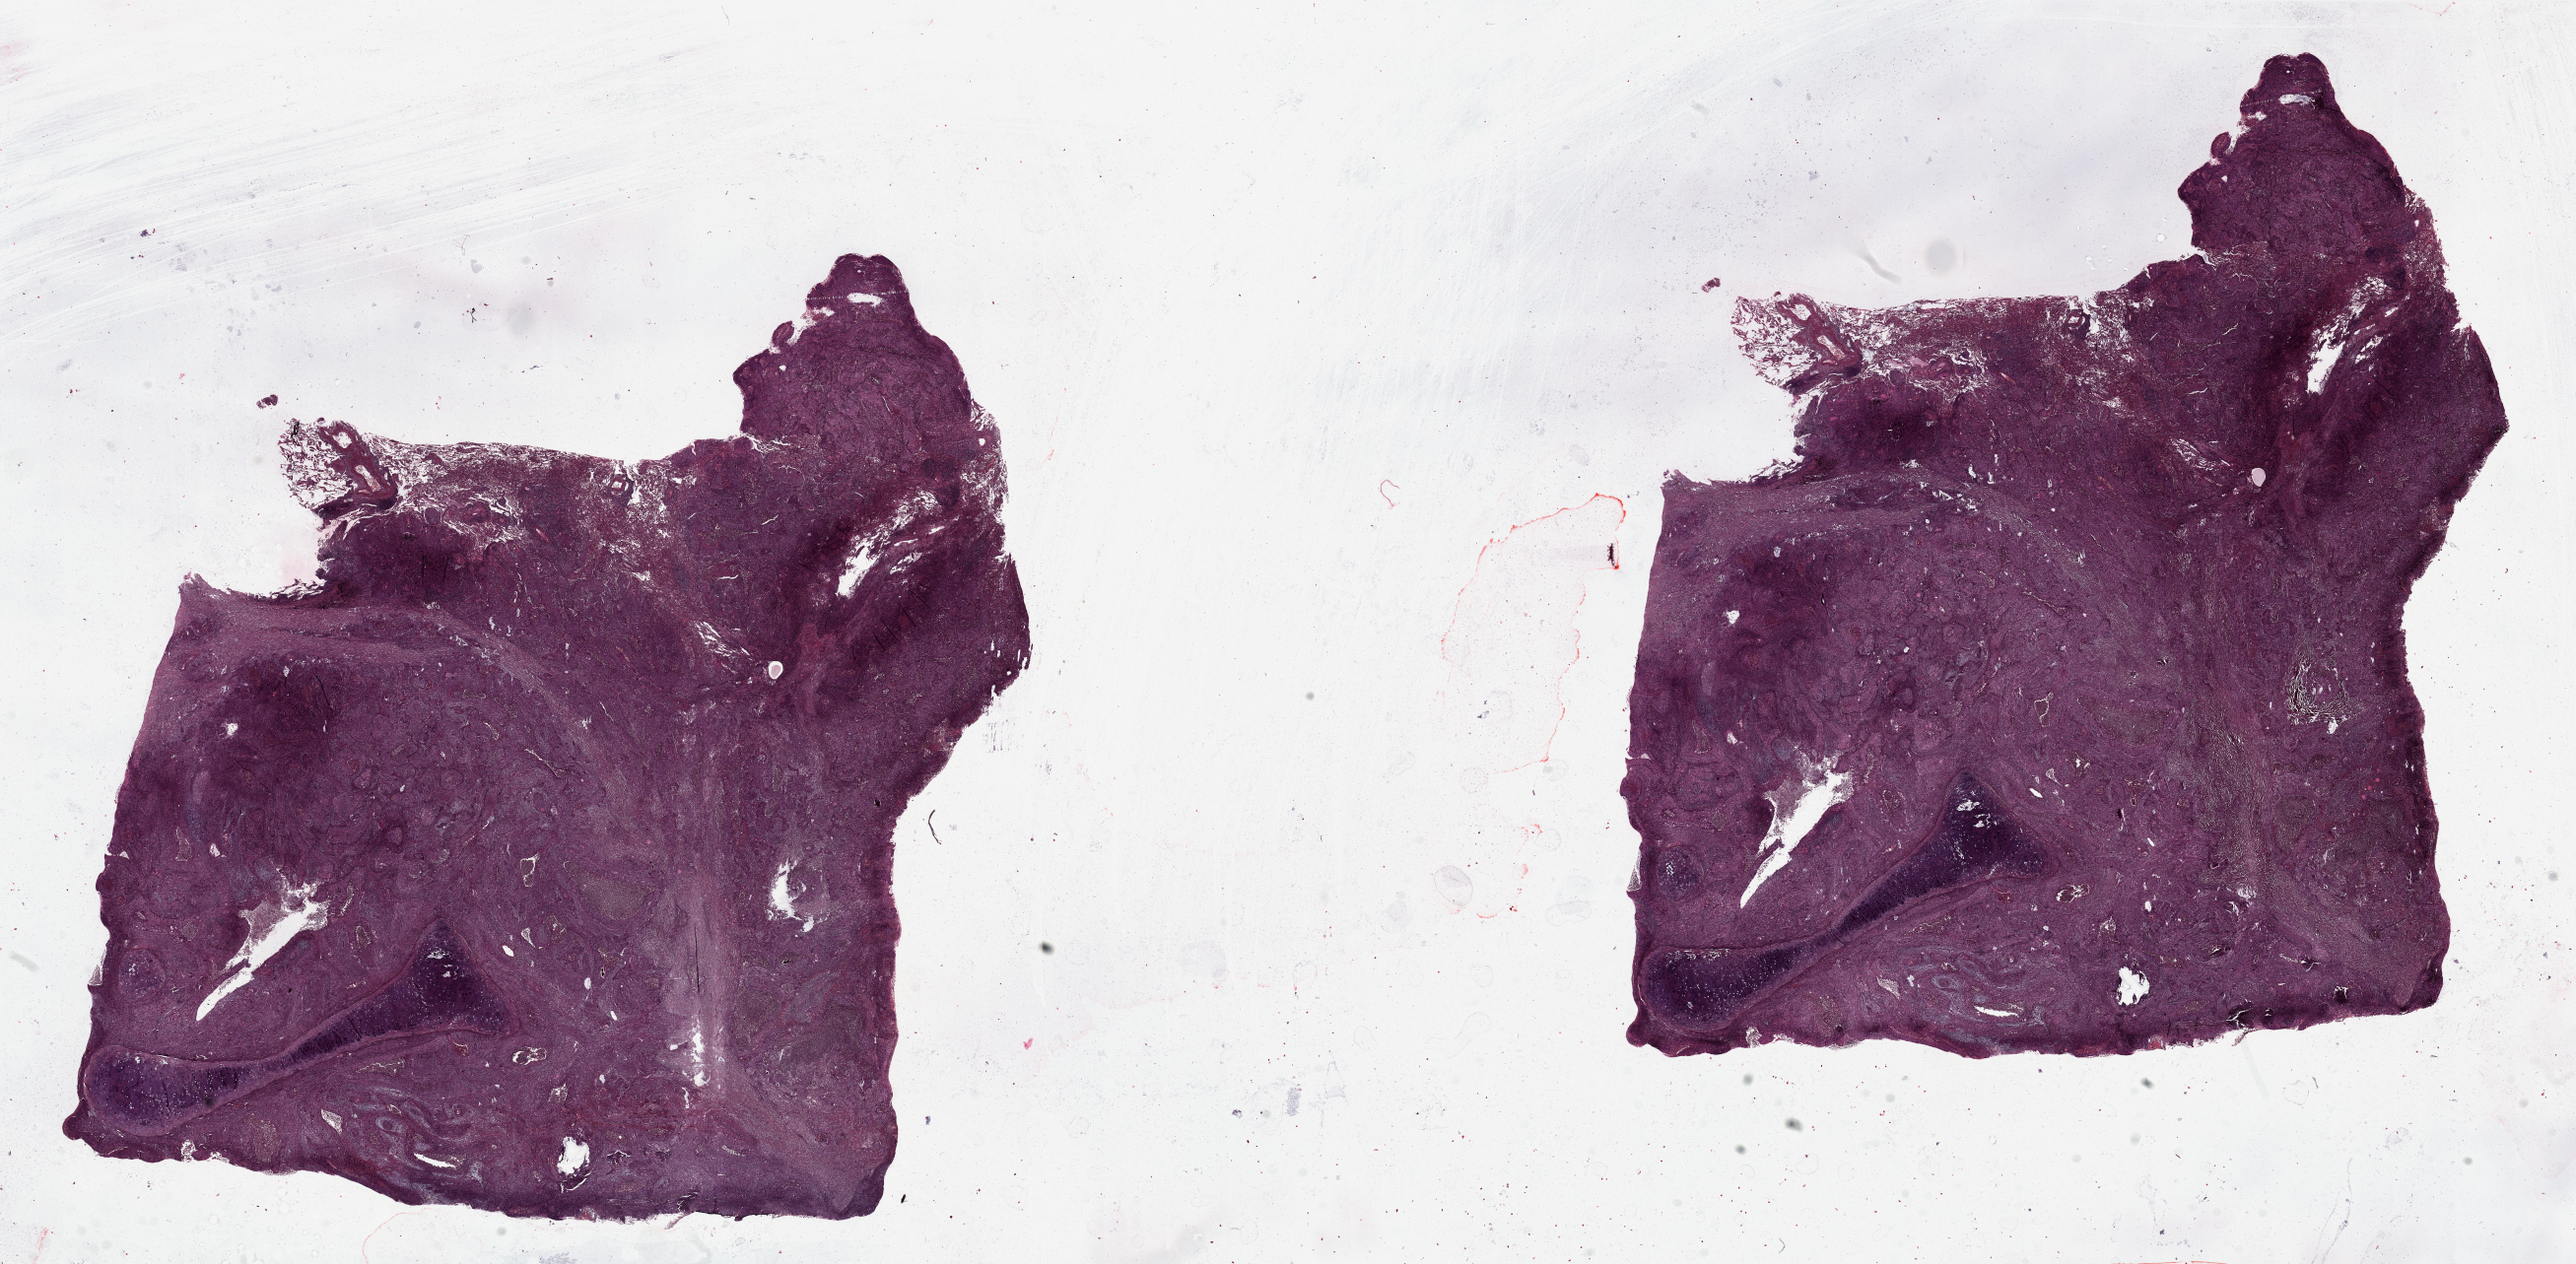
H&E whole-slide image, a low-resolution overview of the entire scanned area, about 41.3 x 20.3 mm (slide scanned at 20x); tumour tissue sample, lung. Male, 66 y/o.
Histologic diagnosis: Squamous cell carcinoma, NOS.